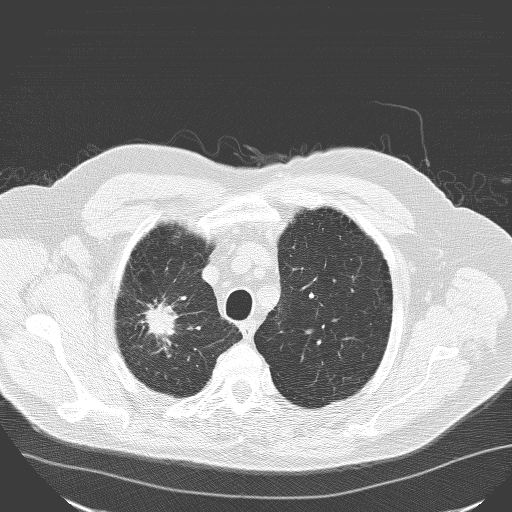
Low-dose screening chest CT, one axial slice. Position 134 of 160 along the scan axis. Lung window (W 1500 / L -600 HU). 3.2 mm slice thickness. 512 × 512 image matrix, field of view 400 × 400 mm.
Outlined on this slice (manually delineated by an expert):
- lesion 1 (tumor, upper lobe of right lung): box from (x=144, y=303) to (x=177, y=337) px